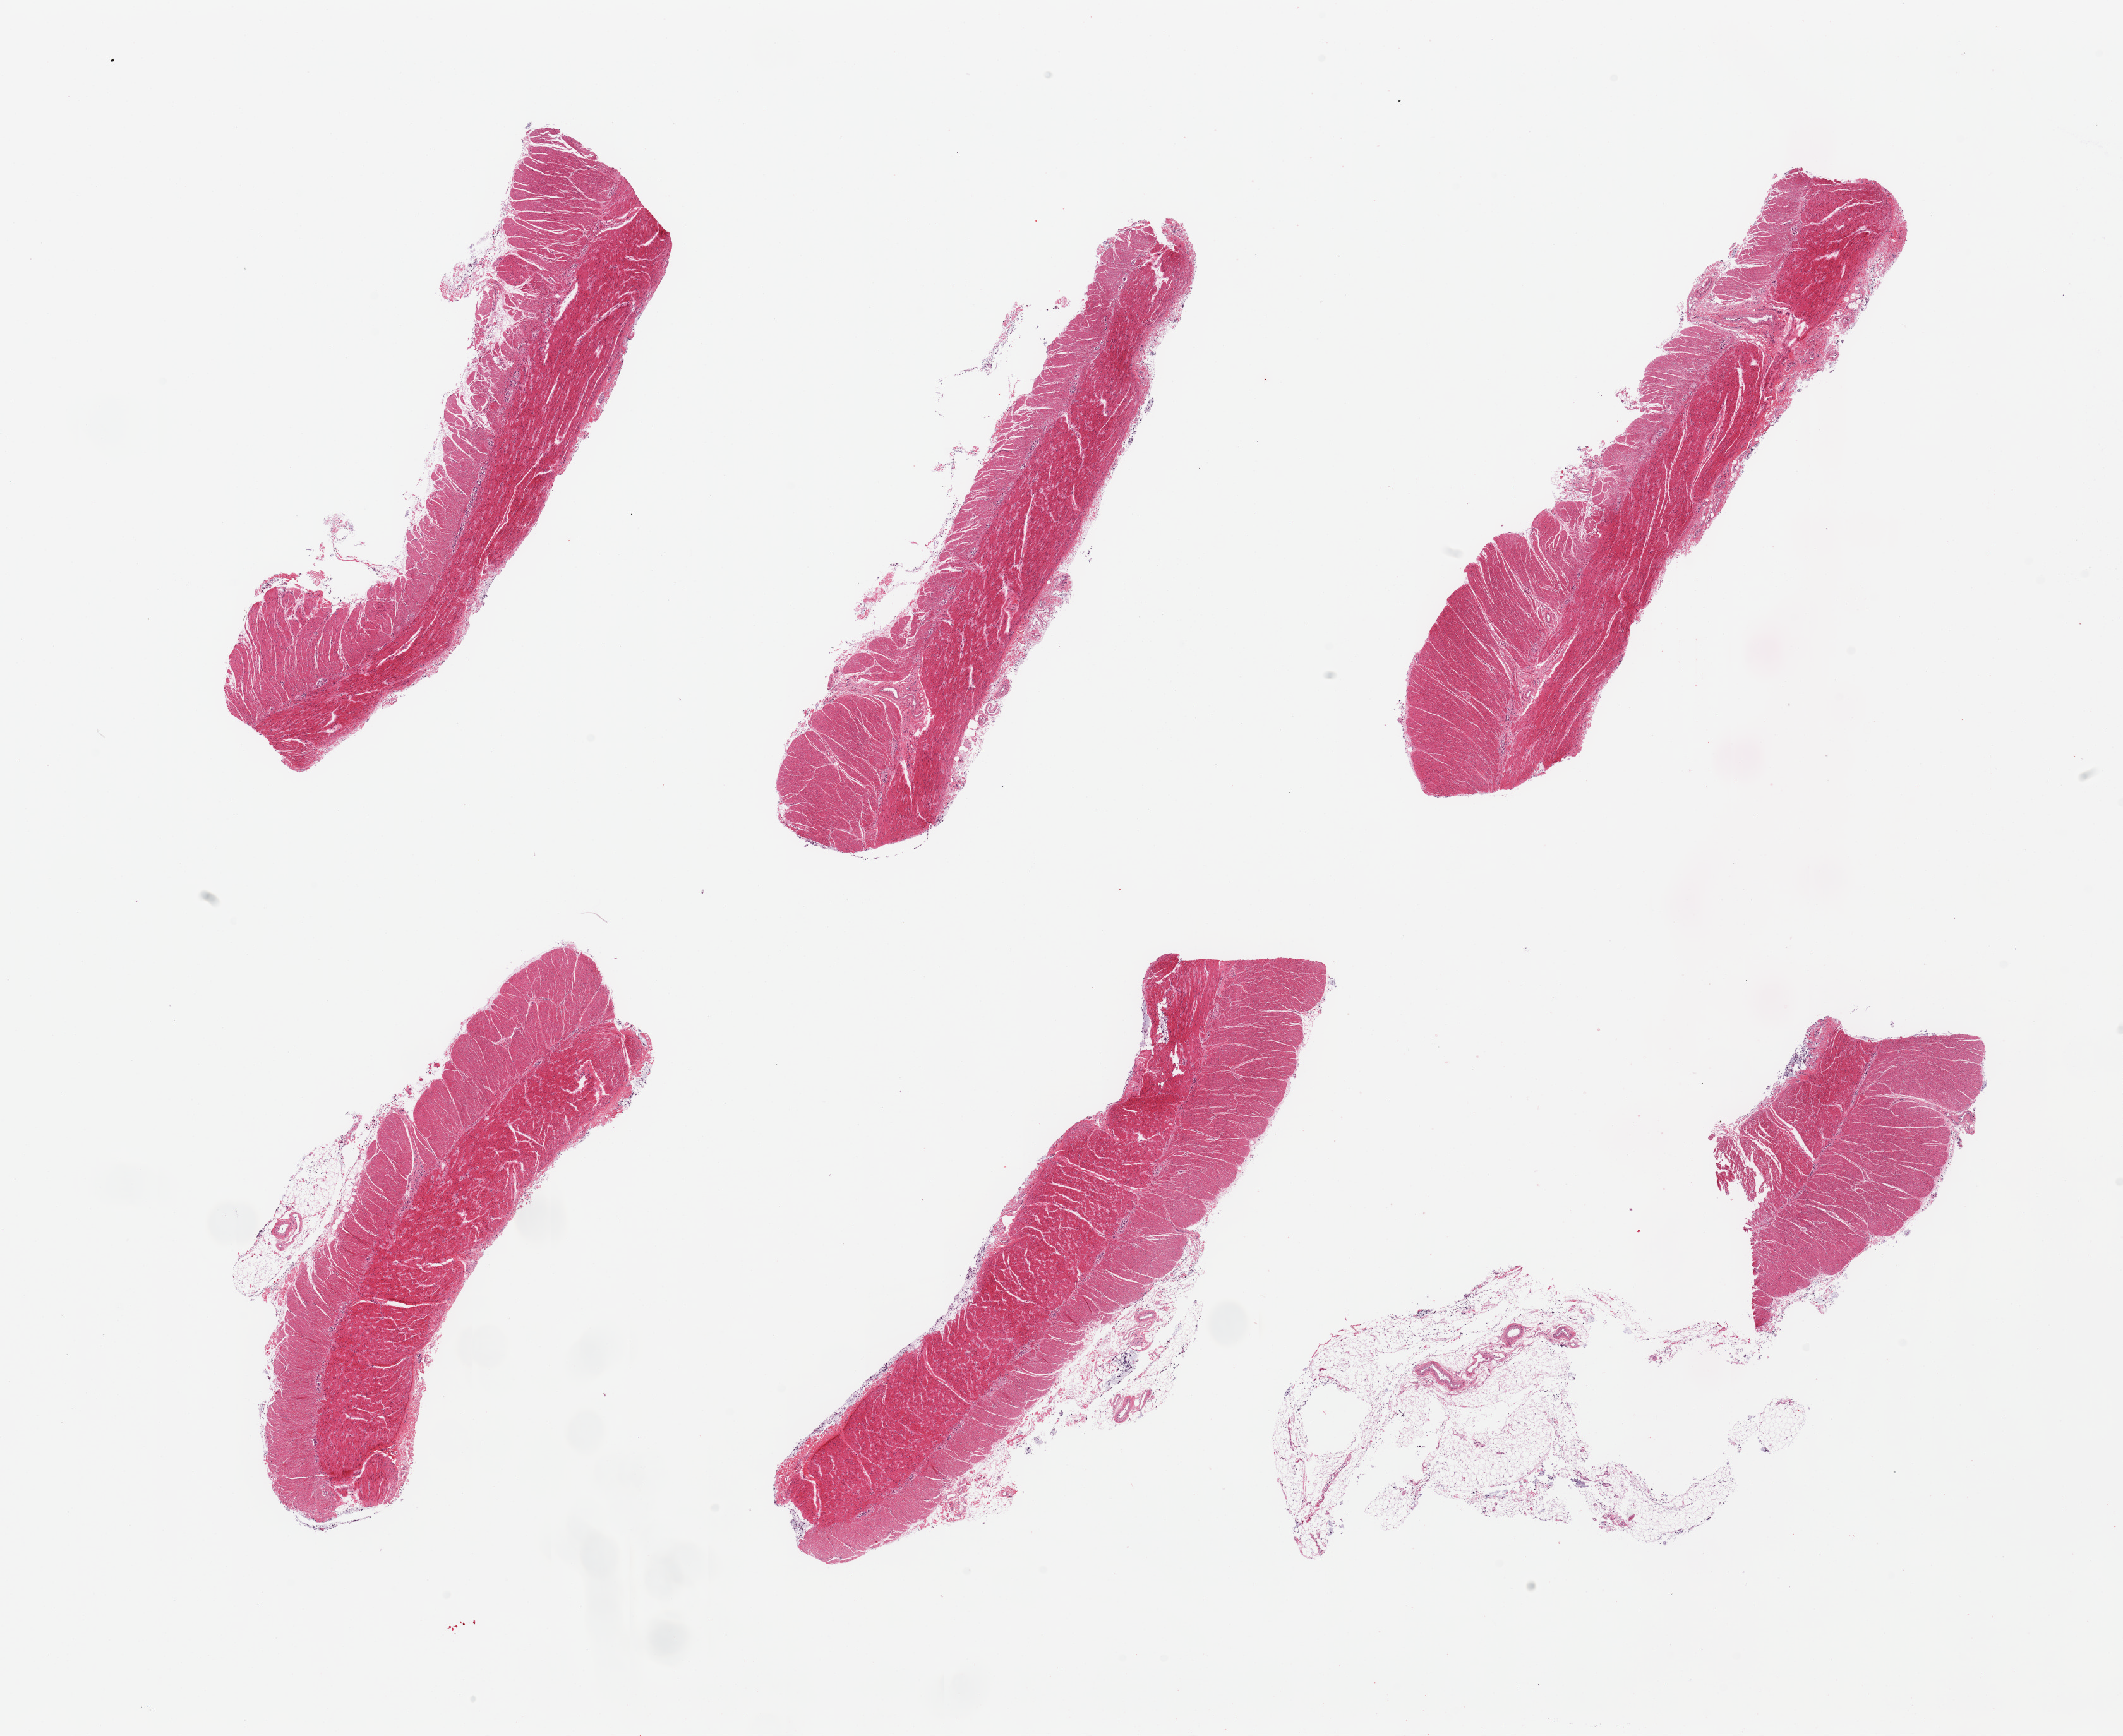
Digitized haematoxylin and eosin-stained section, brightfield — shown as a low-resolution overview of the whole scanned area (about 26.6 x 21.7 mm, slide scanned at 20x), PAXgene-fixed, paraffin-embedded tissue, target tissue: sigmoid colon, tissue donor sample. Female donor.
Review note (as recorded): 6 pieces, confirmed target muscularis, separate fragment of serosal fat.